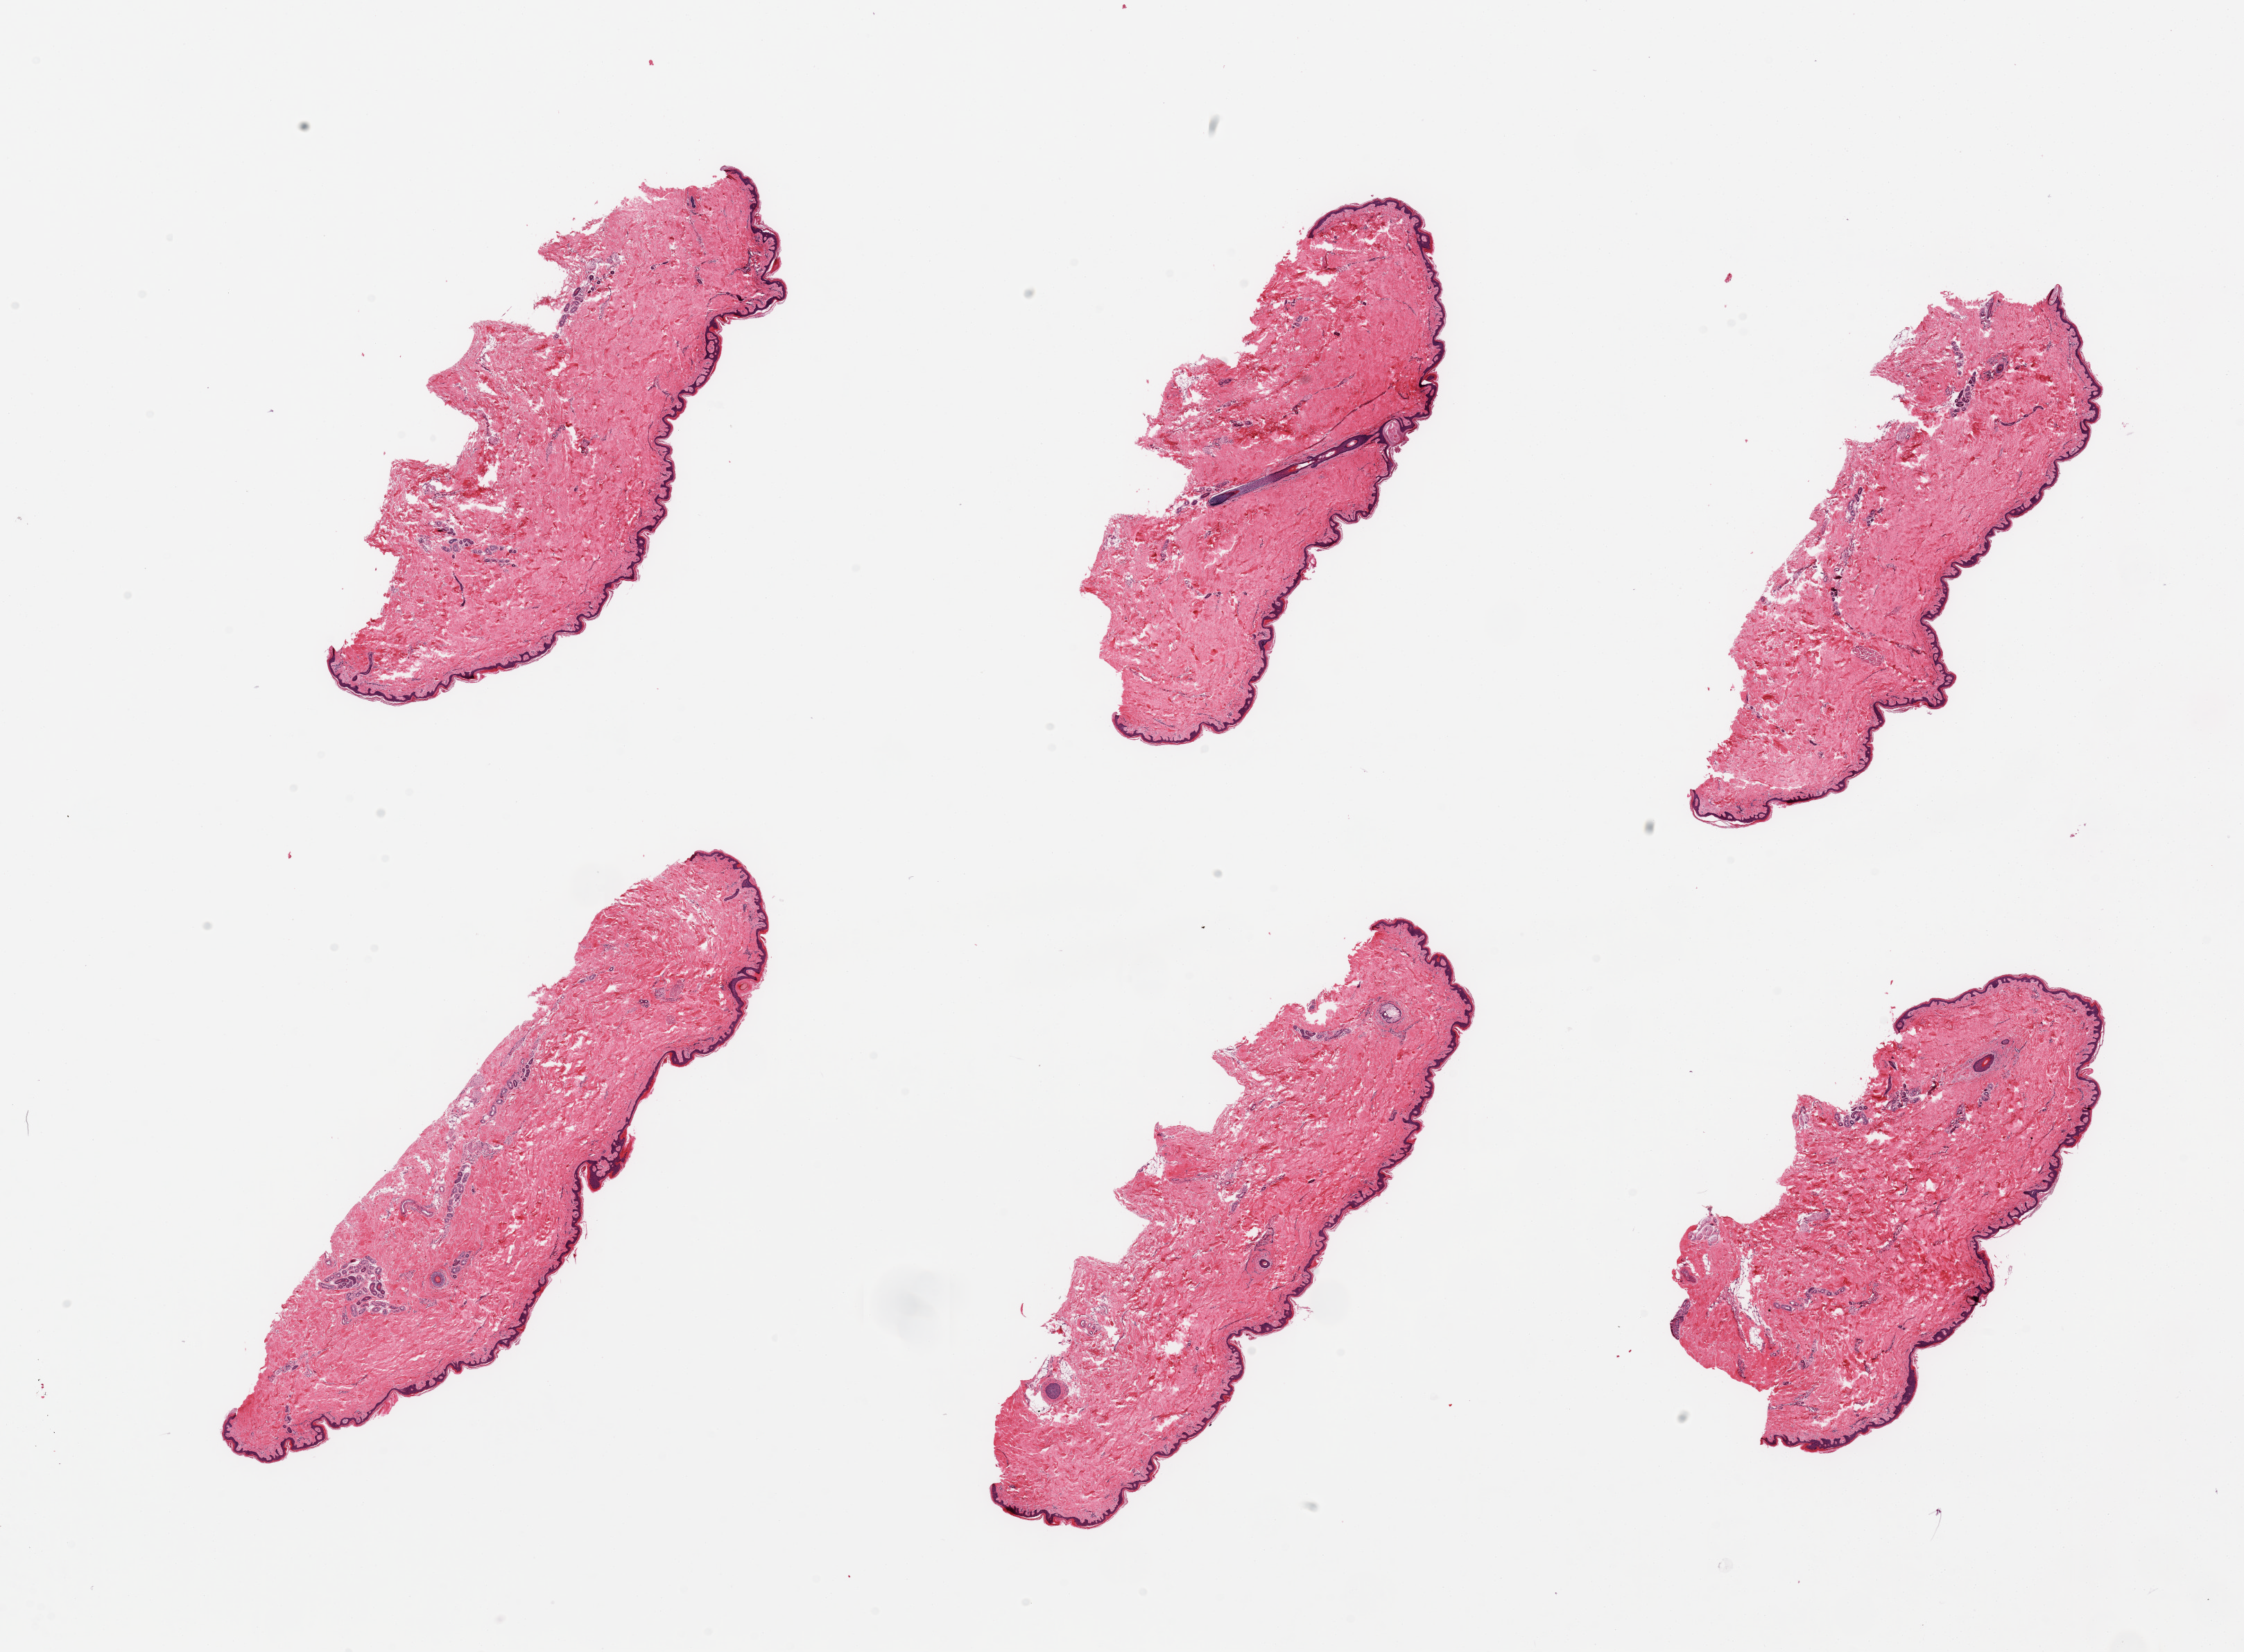
Hematoxylin and eosin (H&E) whole-slide image, brightfield, shown as a low-resolution overview of the whole scanned area (about 25.6 x 18.8 mm, slide scanned at 20x), PAXgene-fixed paraffin-embedded (PFPE) section, section of skin of suprapubic region (target tissue), donor tissue sample.
Reviewer comment on this tissue sample: 6 pieces; well trimmed.